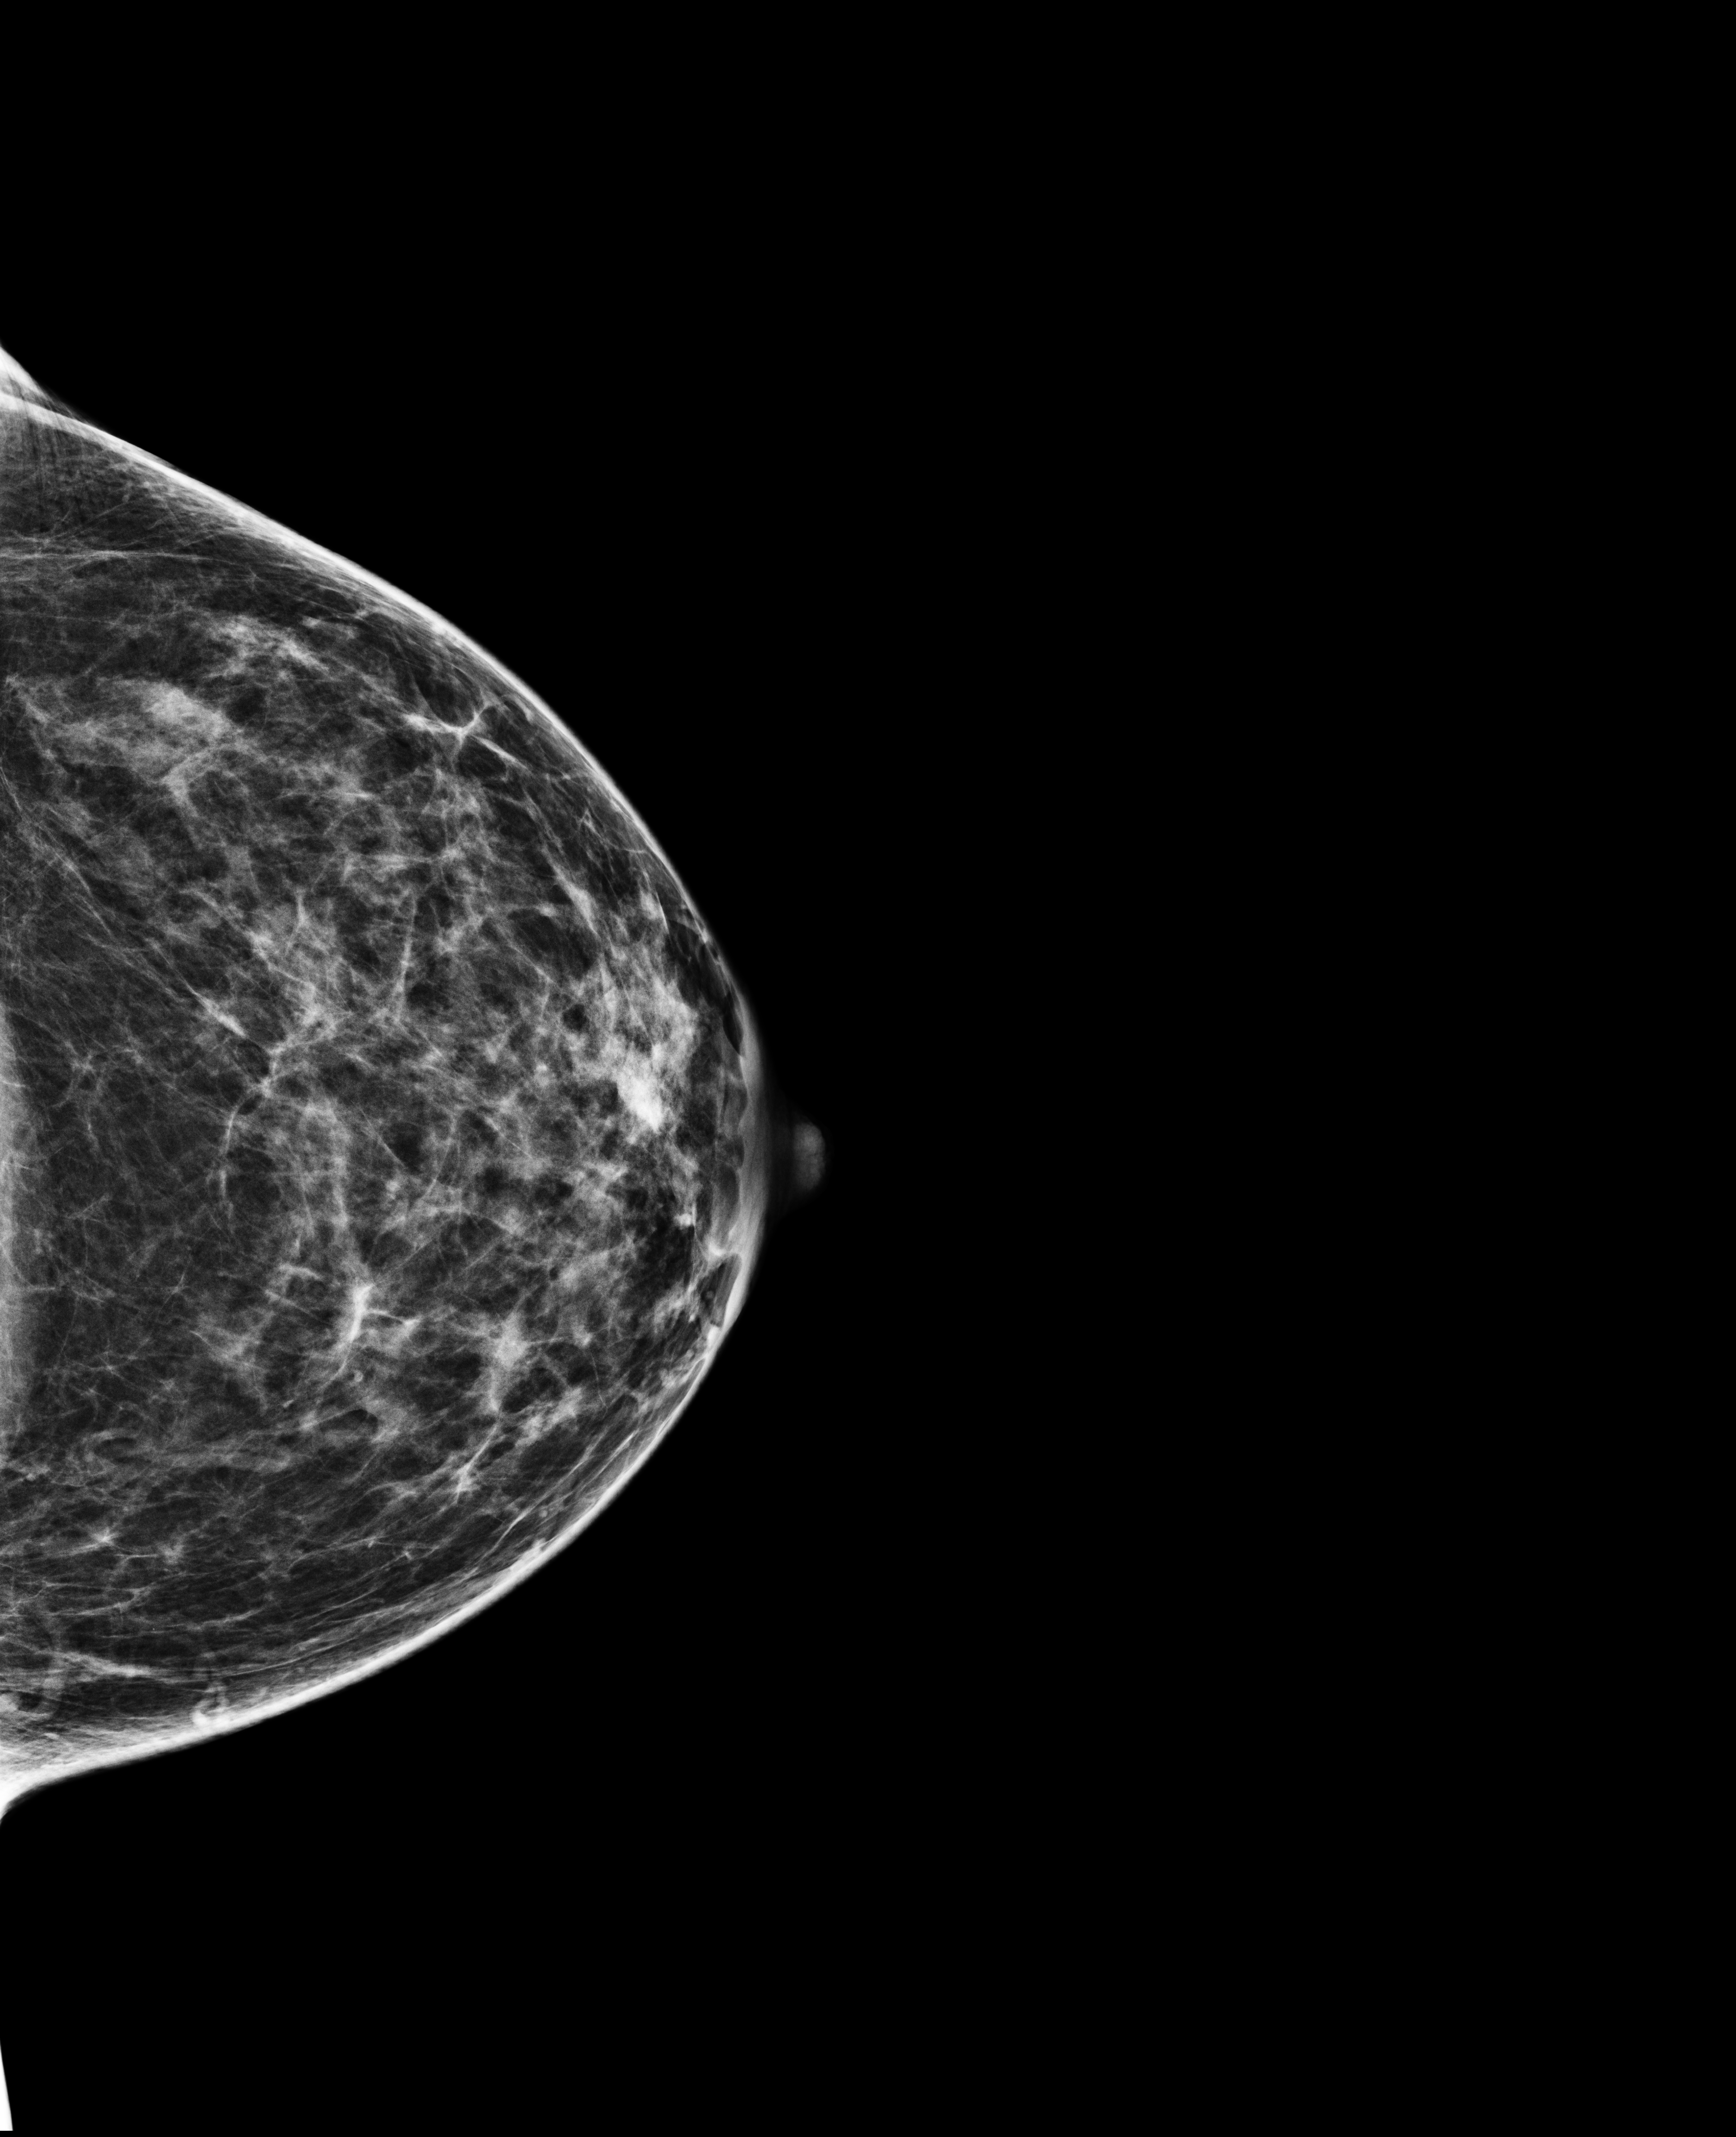
Screening examination. Female patient, age 49 years.
Image type: full-field digital mammogram. Breast: left. Projection: cranio-caudal projection.